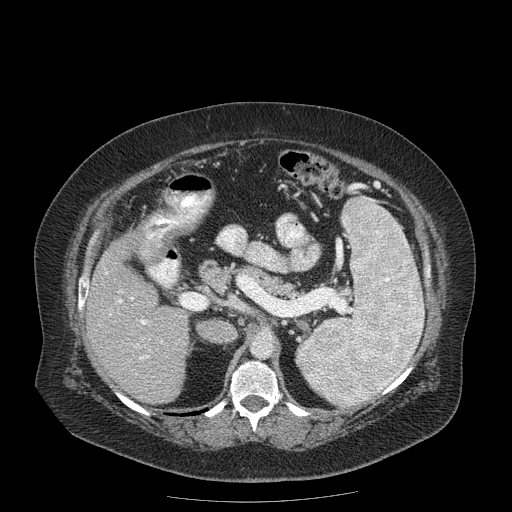
Contrast-enhanced abdominal CT (liver protocol), one axial slice; slice 93 of 204 in the series (ordered by position); reconstruction kernel STANDARD; 120 kVp; soft-tissue window (W 400 / L 40 HU); 512 × 512 image matrix, field of view 440 × 440 mm. Case-level facts recorded for this patient, not image findings: diagnosis: hepatocellular carcinoma (patient treated with transarterial chemoembolisation; whether this scan precedes or follows treatment is not stated here); TNM stage (as recorded): Stage-IIIB; Child-Pugh class: A; tumour differentiation: well differentiated; tumour nodularity: uninodular.
Annotated regions visible in this slice (semi-automatically segmented with operator editing):
- liver parenchyma outside the tumour (the mass and vessels are separate outlines, so this box may not span the whole liver): bounding box (x1, y1, x2, y2) in pixels: (86, 237, 190, 404)
- liver vessels: (106, 272, 162, 360)